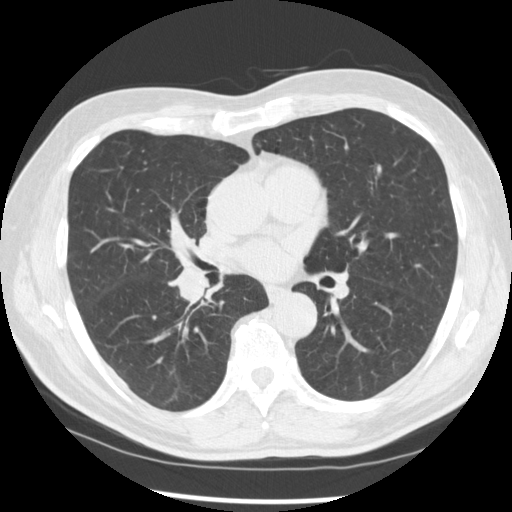
Chest CT (low-dose screening protocol), one axial image. Baseline annual screen. Lung window (W 1500 / L -600 HU). 2.5 mm slice thickness. Standard (soft-tissue) reconstruction kernel (STANDARD). 512 × 512 image matrix, field of view 365 × 365 mm. Male, age 67 years at enrolment.
Expert reader's lesion annotation, bounding box (x1, y1, x2, y2) in pixels: (158, 247, 228, 313). Reader record for this screening exam (exam-level; its link to the box is not recorded): non-calcified nodule or mass ≥4 mm, left lower lobe, 15 × 15 mm, spiculated (stellate) margins, soft tissue attenuation. Note: the box lies in the patient's right hemithorax on this image, whereas the reader's record names the left lung; they may be different findings.